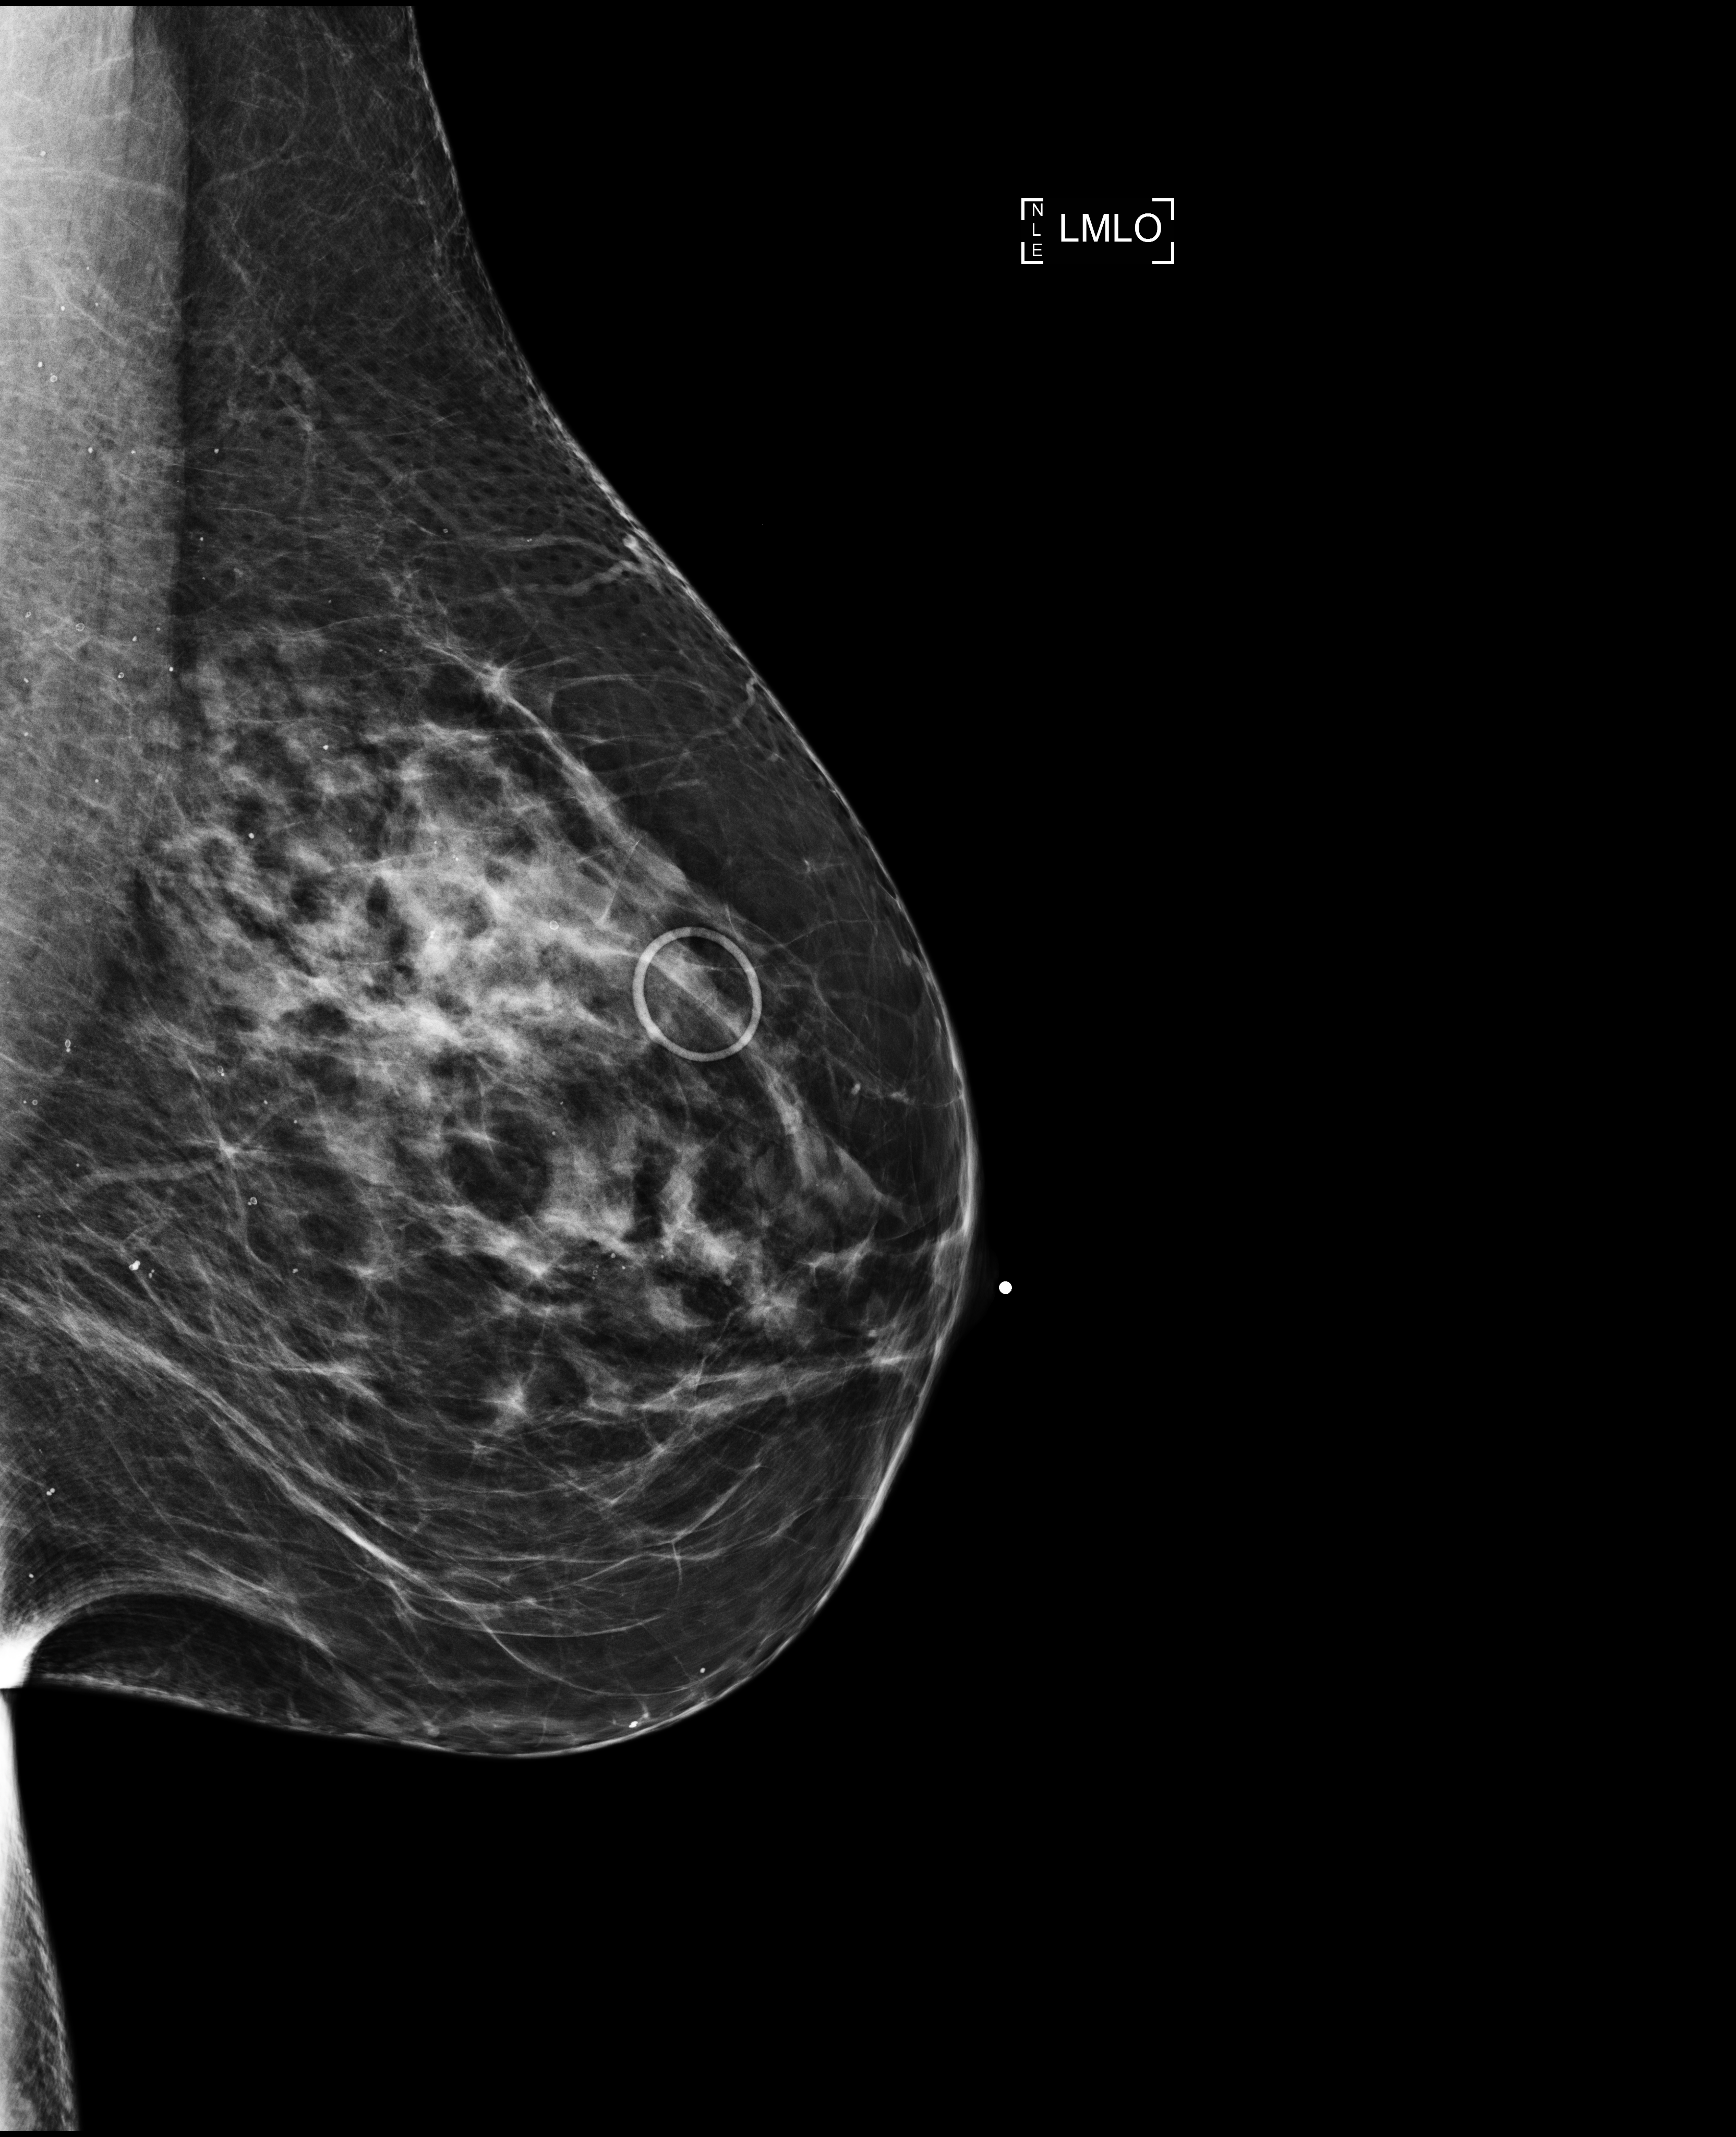
Screening examination; system: Selenia Dimensions. Female patient, age 61 years.
Image type: full-field digital mammogram. Breast: left. Projection: medio-lateral oblique projection.